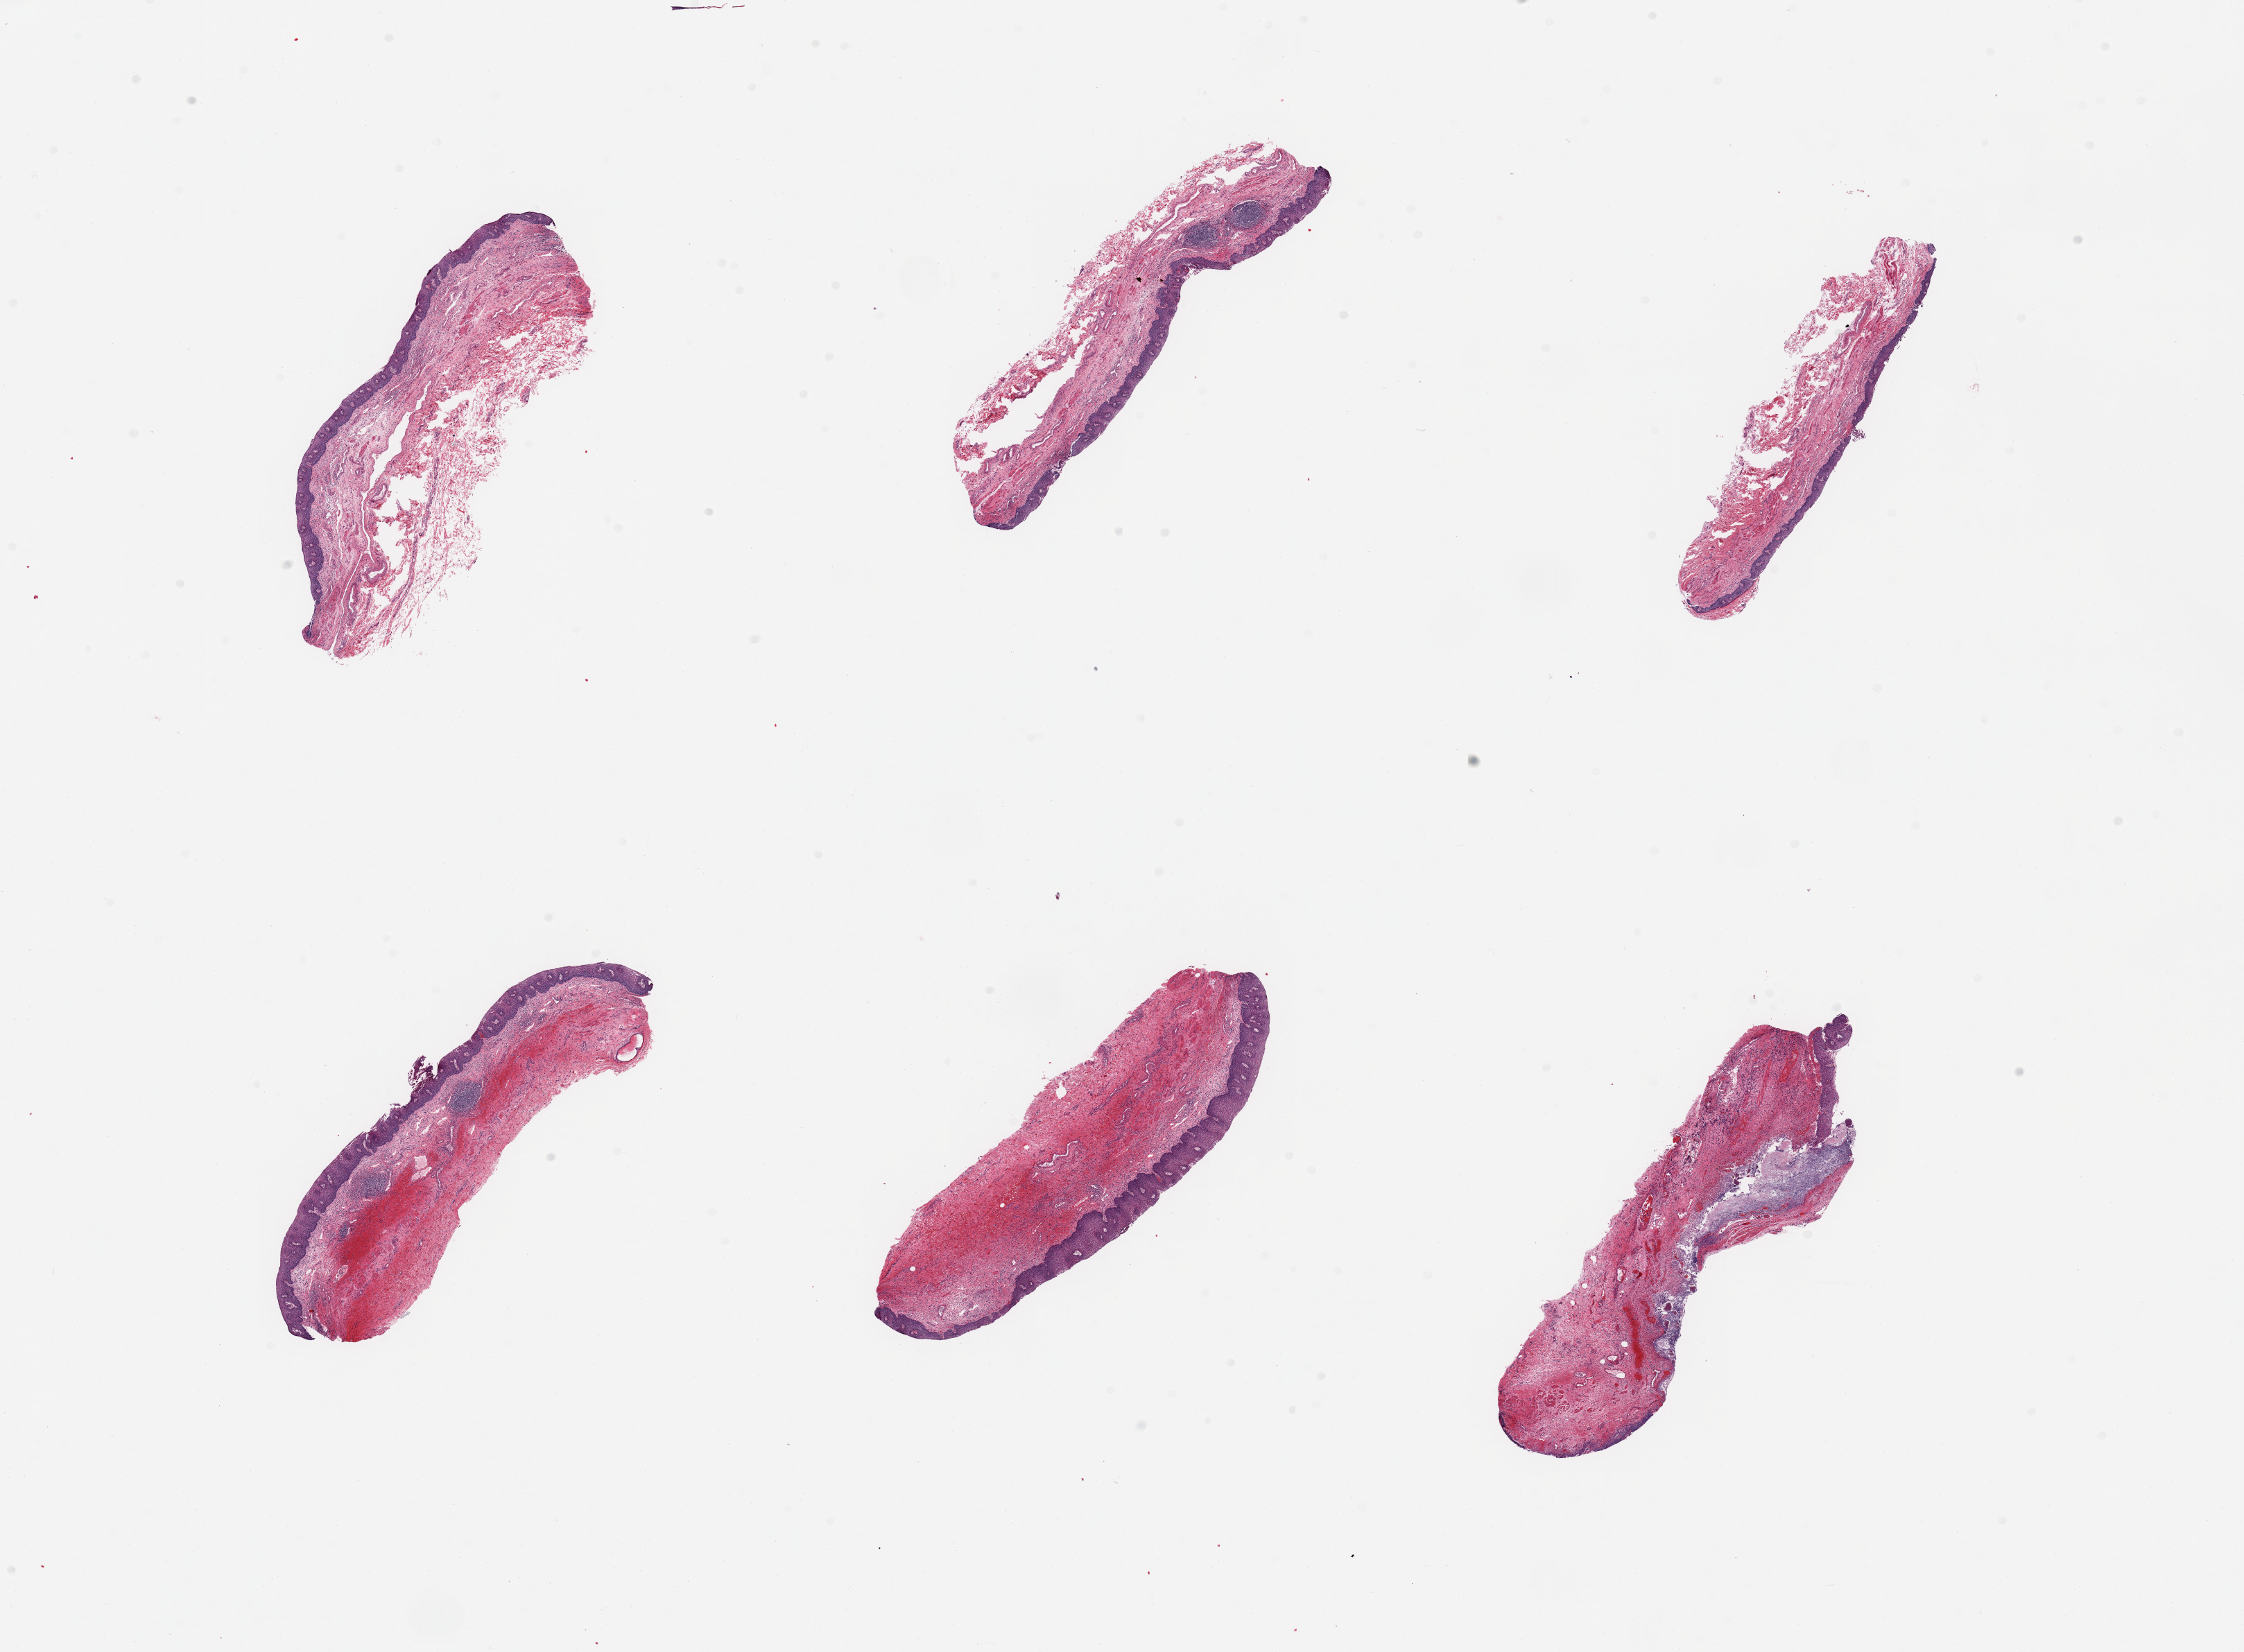
H&E whole-slide image, brightfield — a low-resolution overview of the entire scanned area, about 25.6 x 18.8 mm (acquisition: 20x scan), PAXgene-fixed, paraffin-embedded tissue, section of esophageal mucous membrane (target tissue), tissue donor sample. Donor: male.
Reviewer comment on this tissue sample: 6 pieces; erosive esophagitis, fungal organisms present.